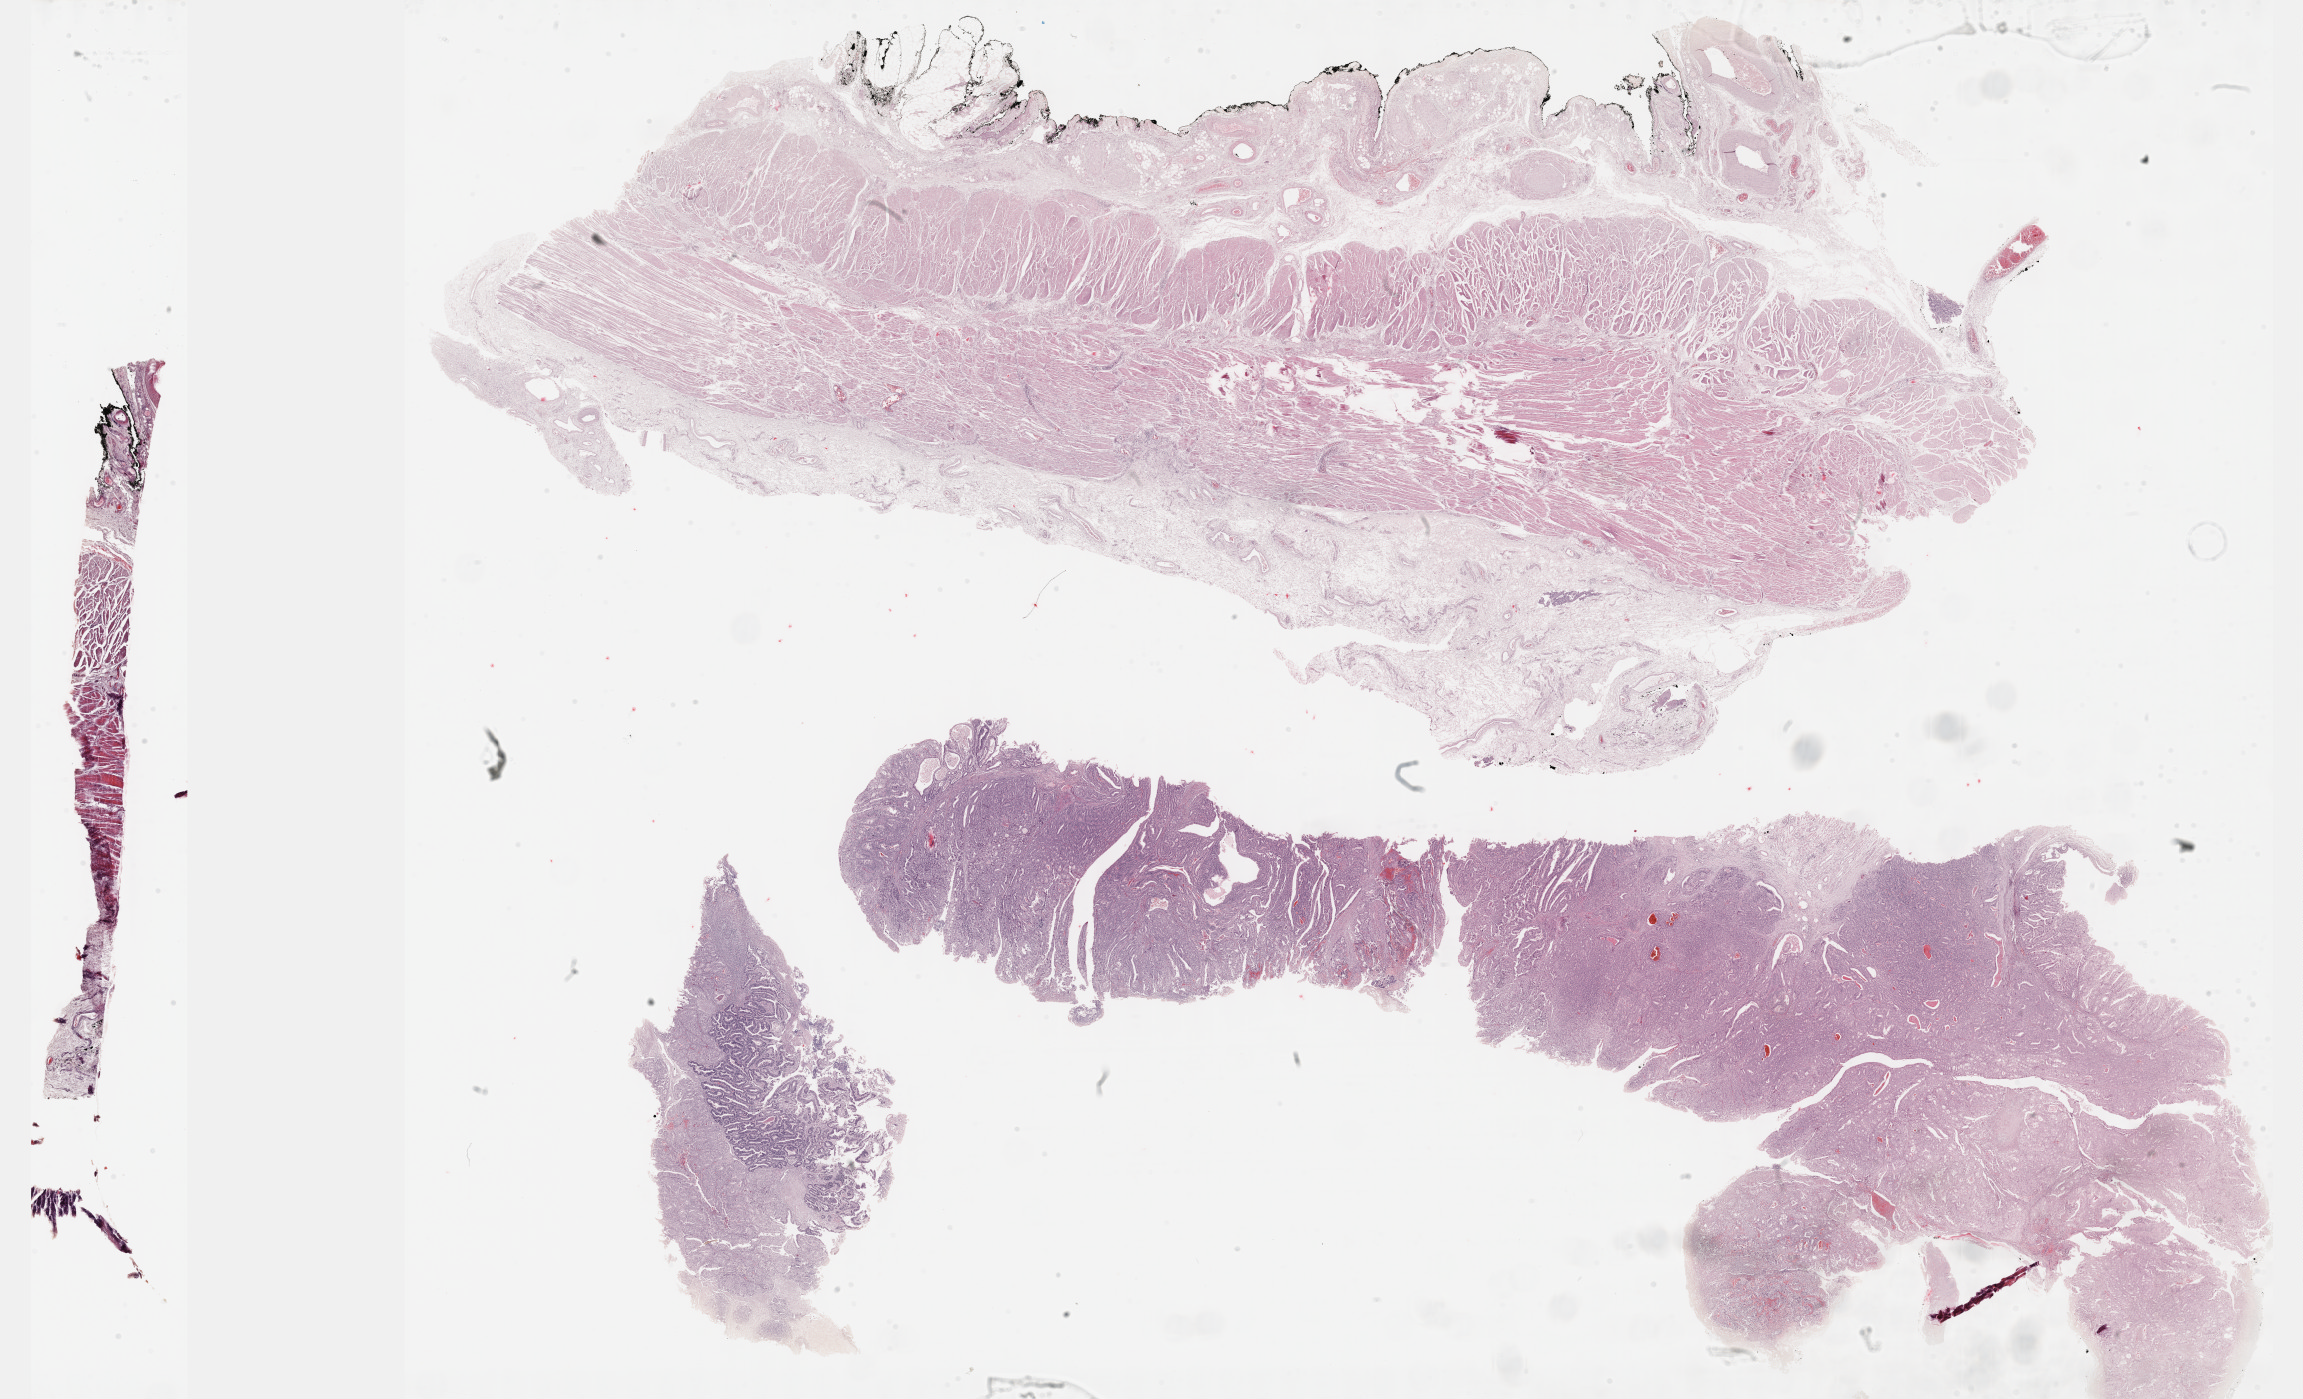
Whole-slide histology image, Hematoxylin and eosin (H&E) stained — low-resolution overview of the scanned area, about 37.2 x 22.6 mm. FFPE section. Primary tumour sample from the esophagus. Male patient; age at initial diagnosis 68 years. Histologic grade: G2 (moderately differentiated).
TNM: T3 N1 M0. Lymph nodes positive (case pathology): 4 of 8 examined. AJCC pathologic stage: III (5th edition). Histologic diagnosis: Adenocarcinoma, NOS (lower third of esophagus).